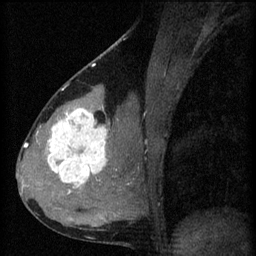
Breast MRI (dynamic contrast-enhanced), one sagittal slice; 3 images stored at this slice position (order not interpretable as contrast timing); 1.5 T; TE 4.2 ms, TR 8.2 ms; 2 mm slice thickness; 256 × 256 image matrix, field of view 180 × 180 mm. Female patient, age 37 years.
Outlined on this slice (semi-automatically segmented with operator editing):
- analysis volume of interest (the breast-tissue region the enhancement analysis was run in; not a lesion): bounding box (x1, y1, x2, y2) in pixels: (44, 100, 119, 197)
- tumour enhancement mask (voxels above the 70 % enhancement threshold inside the analysis volume of interest): (48, 108, 109, 195)